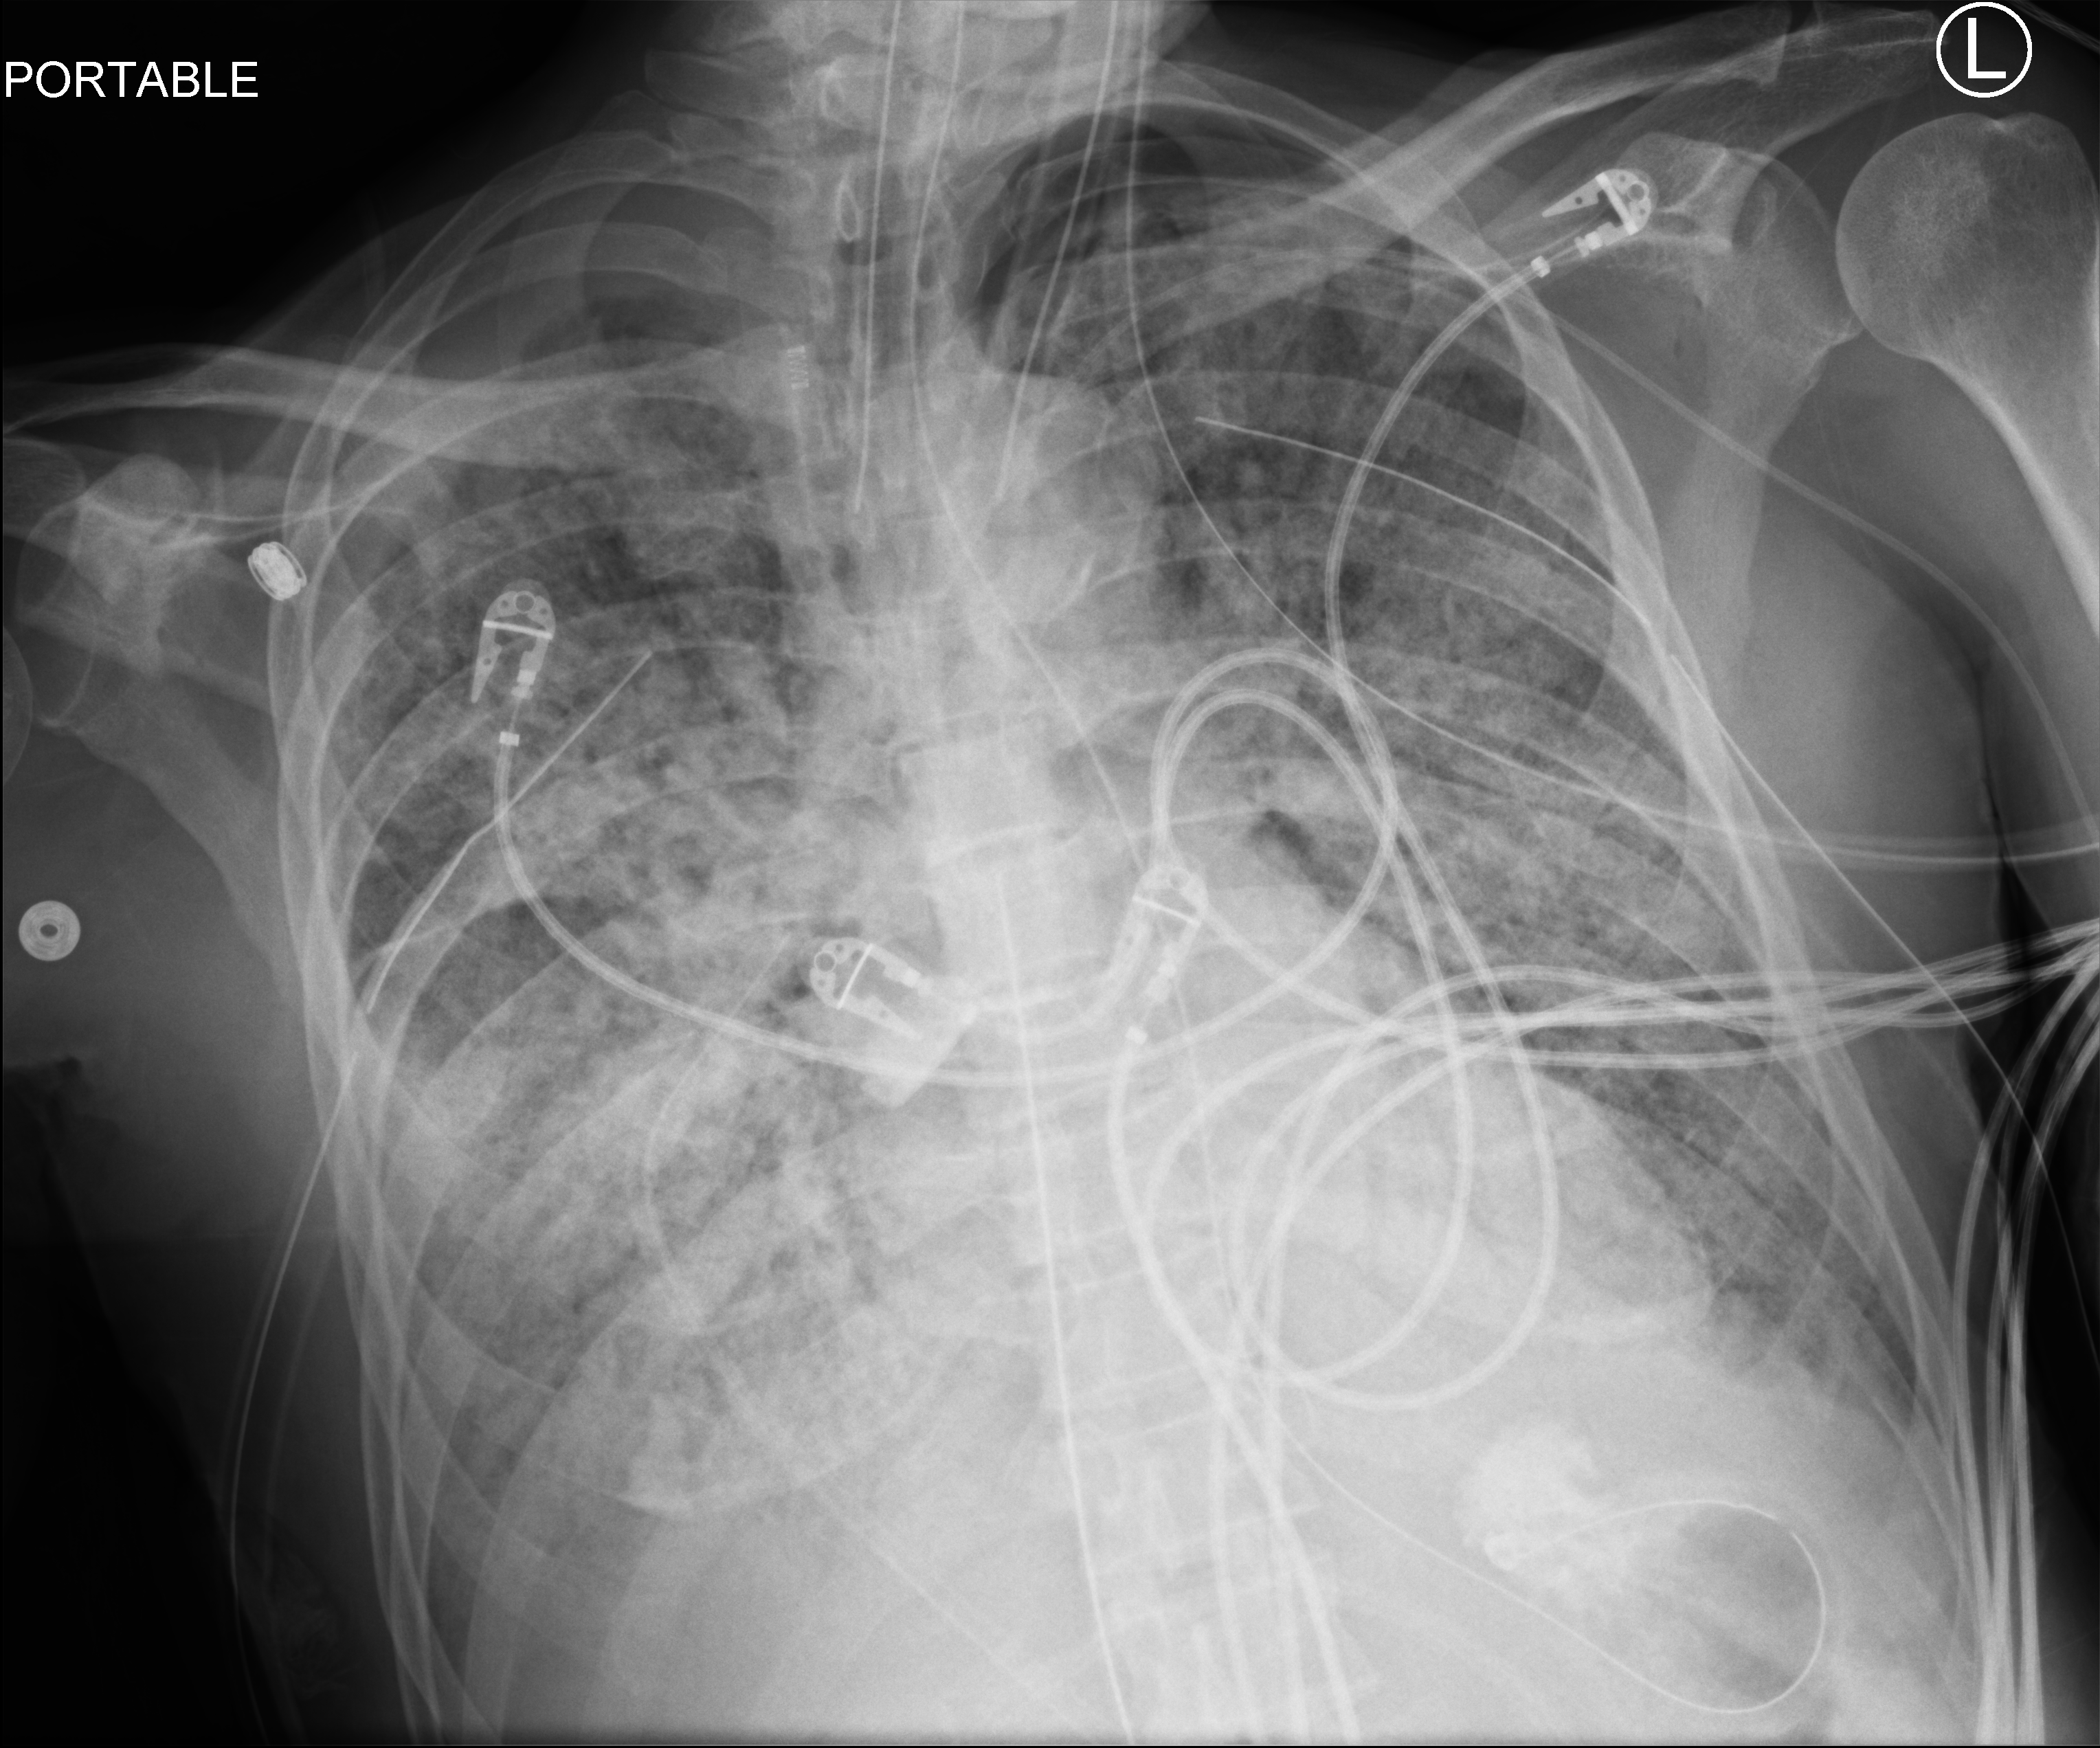
Portable chest radiograph; anteroposterior (AP) projection. Patient hospitalised with COVID-19; male, aged 60–74 years.
Admission-level facts for this patient (not findings on this image; timing relative to this image not recorded):
- admitted to intensive care during this hospital stay: yes
- mechanically ventilated during this hospital stay: yes